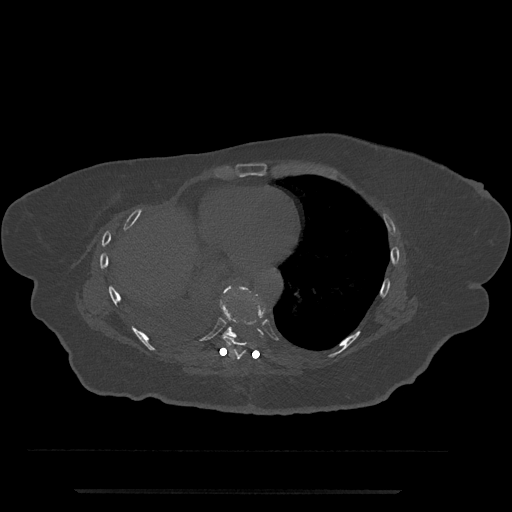
CT including the spine, one axial slice. Position 374 of 797 along the scan axis. Reconstruction kernel Br40s/3. 120 kVp. Bone window (W 1800 / L 400 HU). 0.5 mm slice thickness. 512 × 512 image matrix. Female patient, age 51 years. Case-level facts recorded for this patient, not image findings: primary cancer: neuro; vertebrae with lytic lesions (as recorded): T8.
Structures marked on this image (semi-automatically segmented with operator editing):
- T8 vertebra: bounding box [x1, y1, x2, y2] px = [222, 297, 265, 360]
- T9 vertebra: [218, 285, 264, 339]